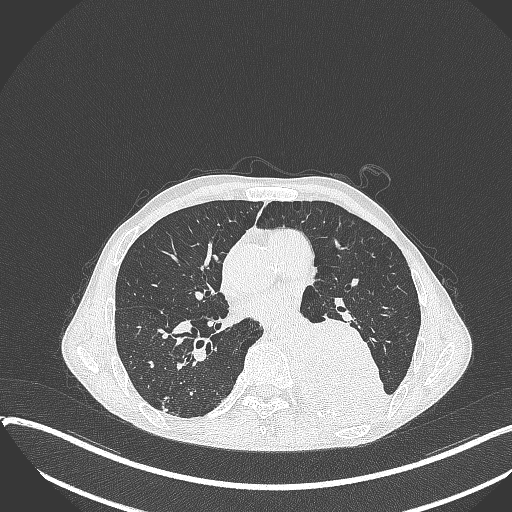
Chest CT, one axial slice. Slice 180 of 401 in the series (ordered by position). Reconstruction kernel B70f. 120 kVp. Lung window (W 1500 / L -600 HU). 1 mm slice thickness. 512 × 512 image matrix, field of view 400 × 400 mm. Patient: male, 57 years. From the clinical record (not read from this slice): clinical TNM (as recorded): T4 N0 M0.
Structures marked on this image (bounding box drawn by a radiologist):
- lung tumour (recorded histology: squamous cell carcinoma): bounding box <302,314,390,432> (left, top, right, bottom; pixels)